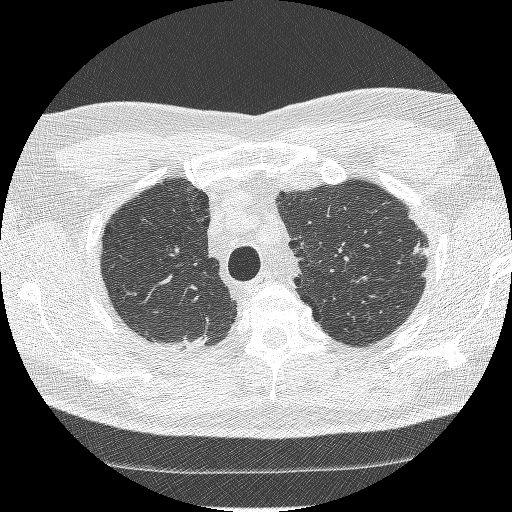
Chest CT (low-dose screening protocol), one axial image. Baseline screening round. Lung window (W 1500 / L -600 HU). 1.25 mm slice thickness. Lung (sharp) reconstruction kernel (BONE). Slice 222 of 260 in the series. Male participant, aged 66 years at enrolment. Current smoker at enrolment.
Expert-annotated lung lesion, bounding box [x1, y1, x2, y2] px = [398, 235, 435, 271]. Reader record for this screening exam (exam-level; its link to the box is not recorded): non-calcified nodule or mass ≥4 mm, right lower lobe, 45 × 19 mm, spiculated (stellate) margins, soft tissue attenuation. Note: the box lies in the patient's left hemithorax on this image, whereas the reader's record names the right lung; they may be different findings. Lung cancer was diagnosed 960 days after this screen (after the third annual screen): adenocarcinoma, NOS, left upper lobe, poorly differentiated (G3), stage IB (AJCC 6th edition), 16 mm at pathology.